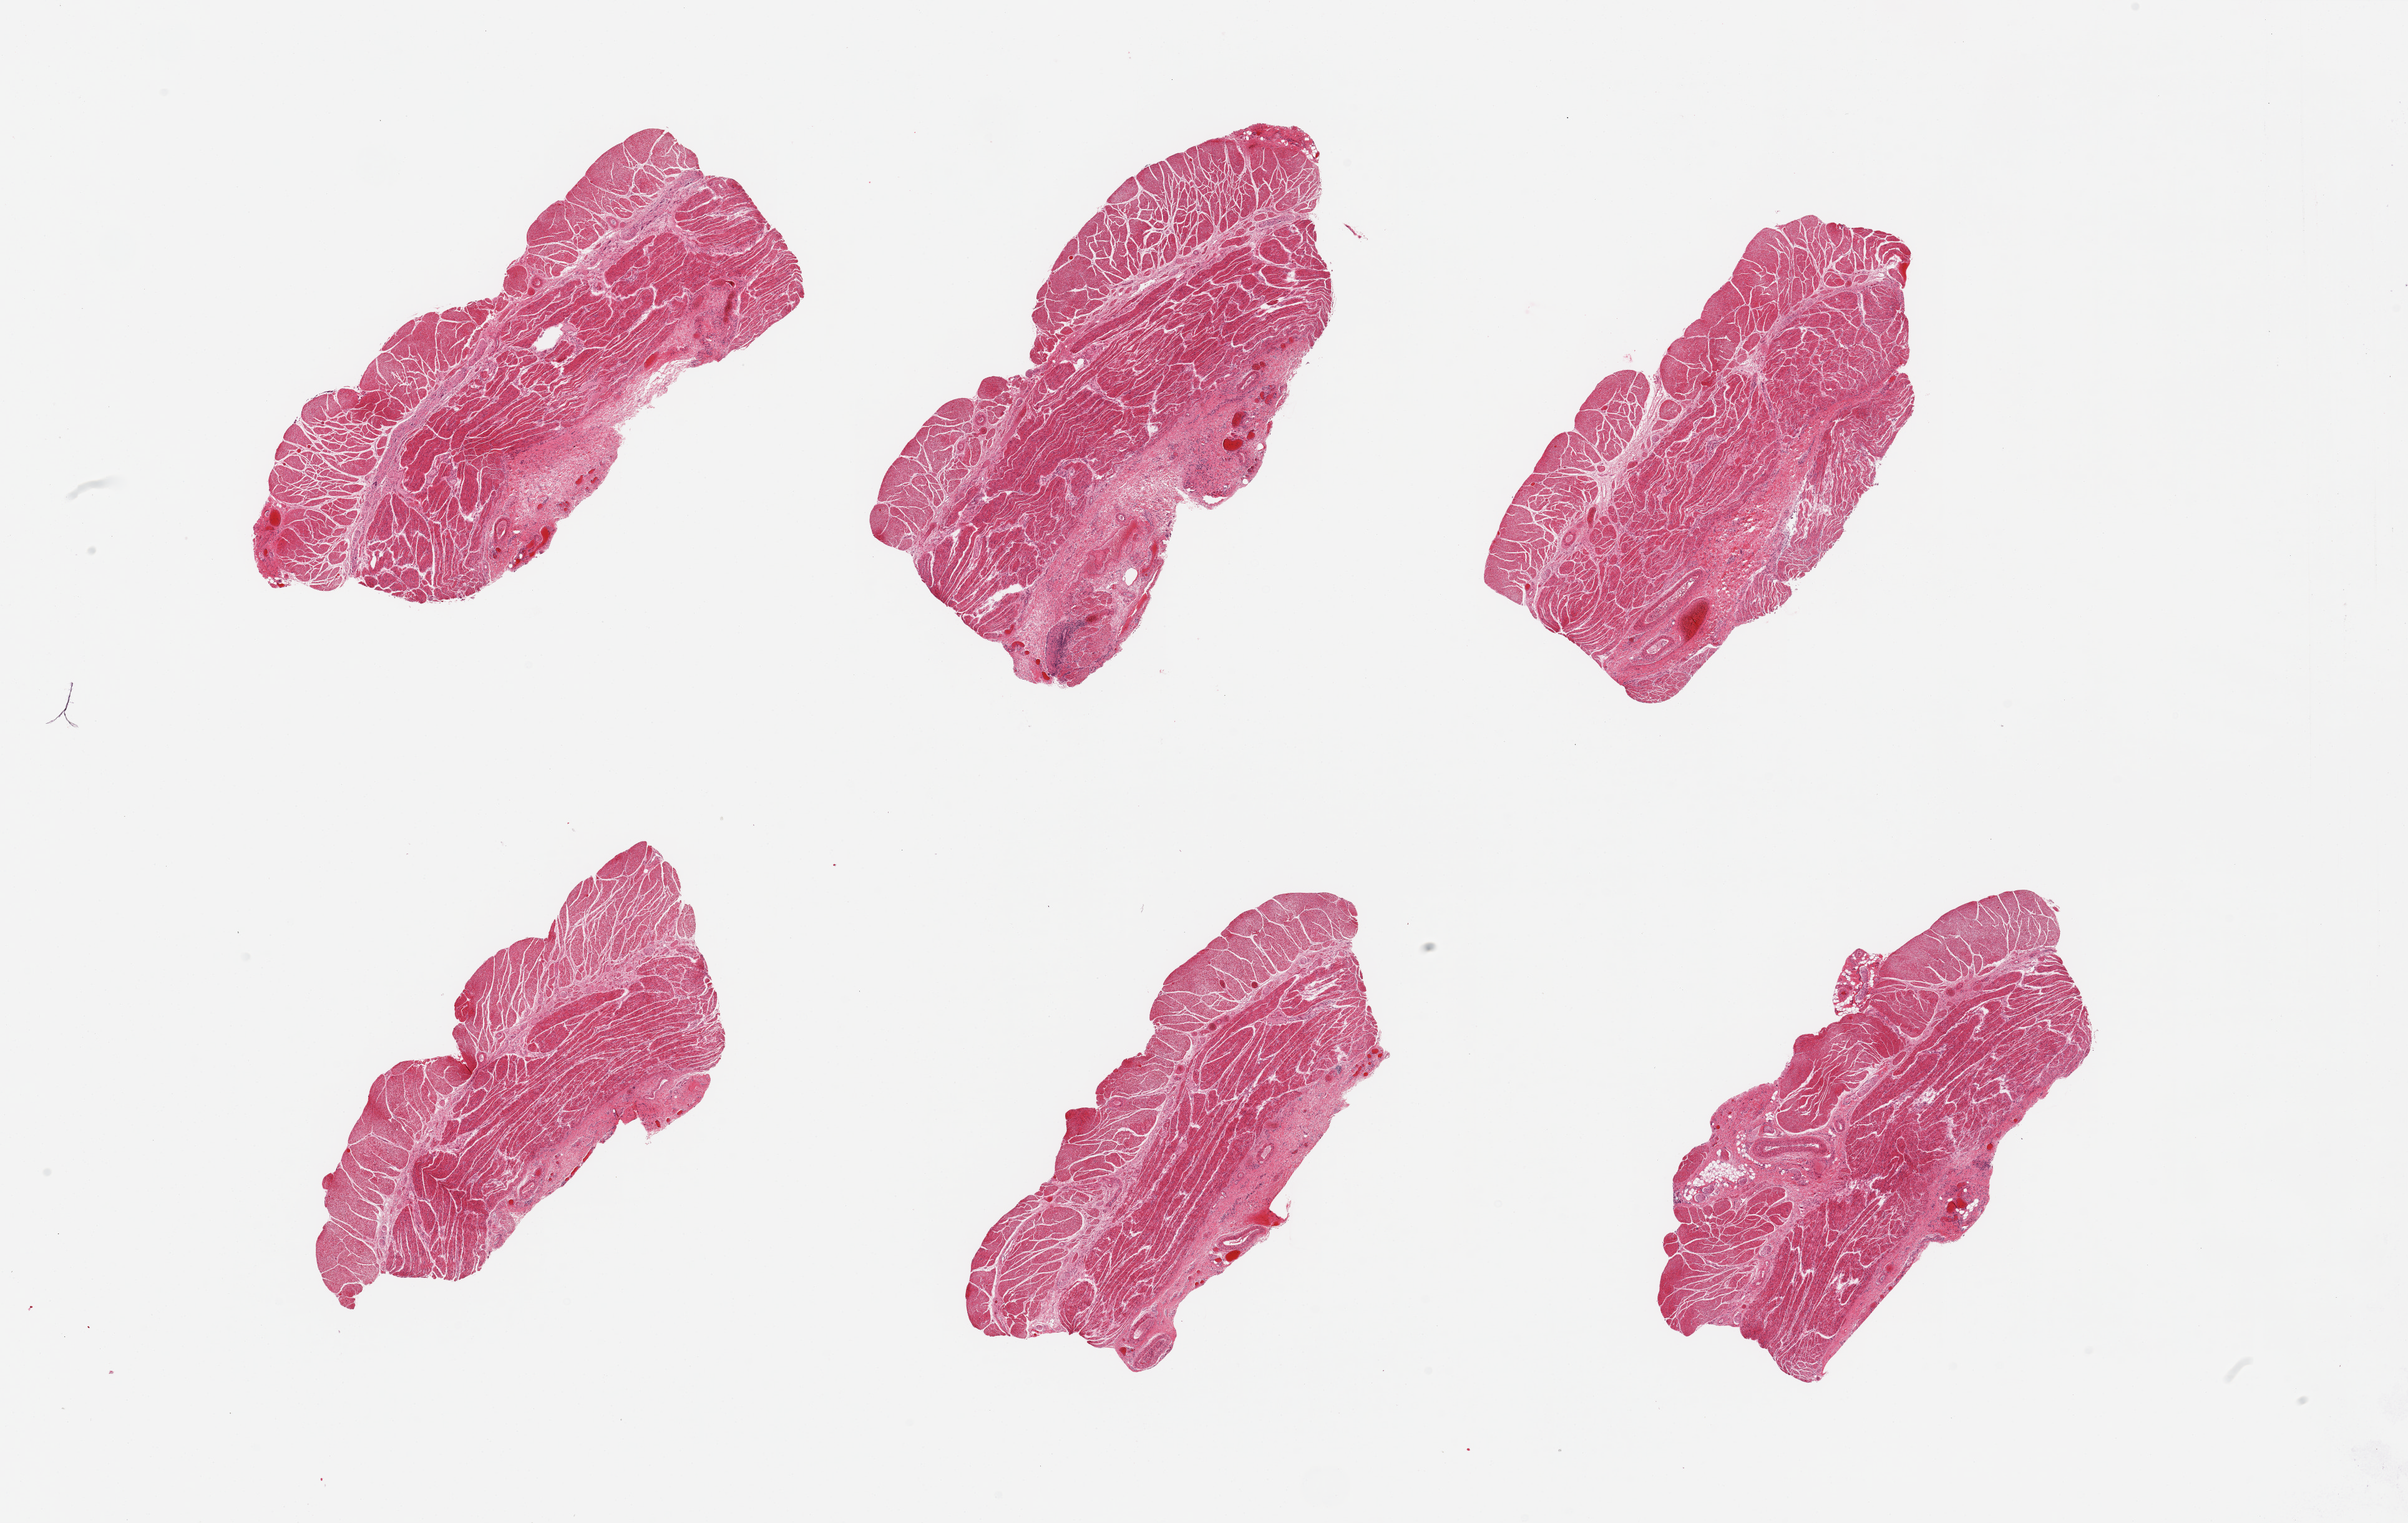
Digitized hematoxylin and eosin (H&E)-stained section, brightfield, a low-resolution overview of the entire scanned area, about 30.5 x 19.3 mm; PAXgene-fixed paraffin-embedded (PFPE) section; sampled site (target tissue): esophageal muscle; donor tissue sample. Donor: male.
• review note (as recorded): 6 pieces, all muscularis, unusually poorly preserved